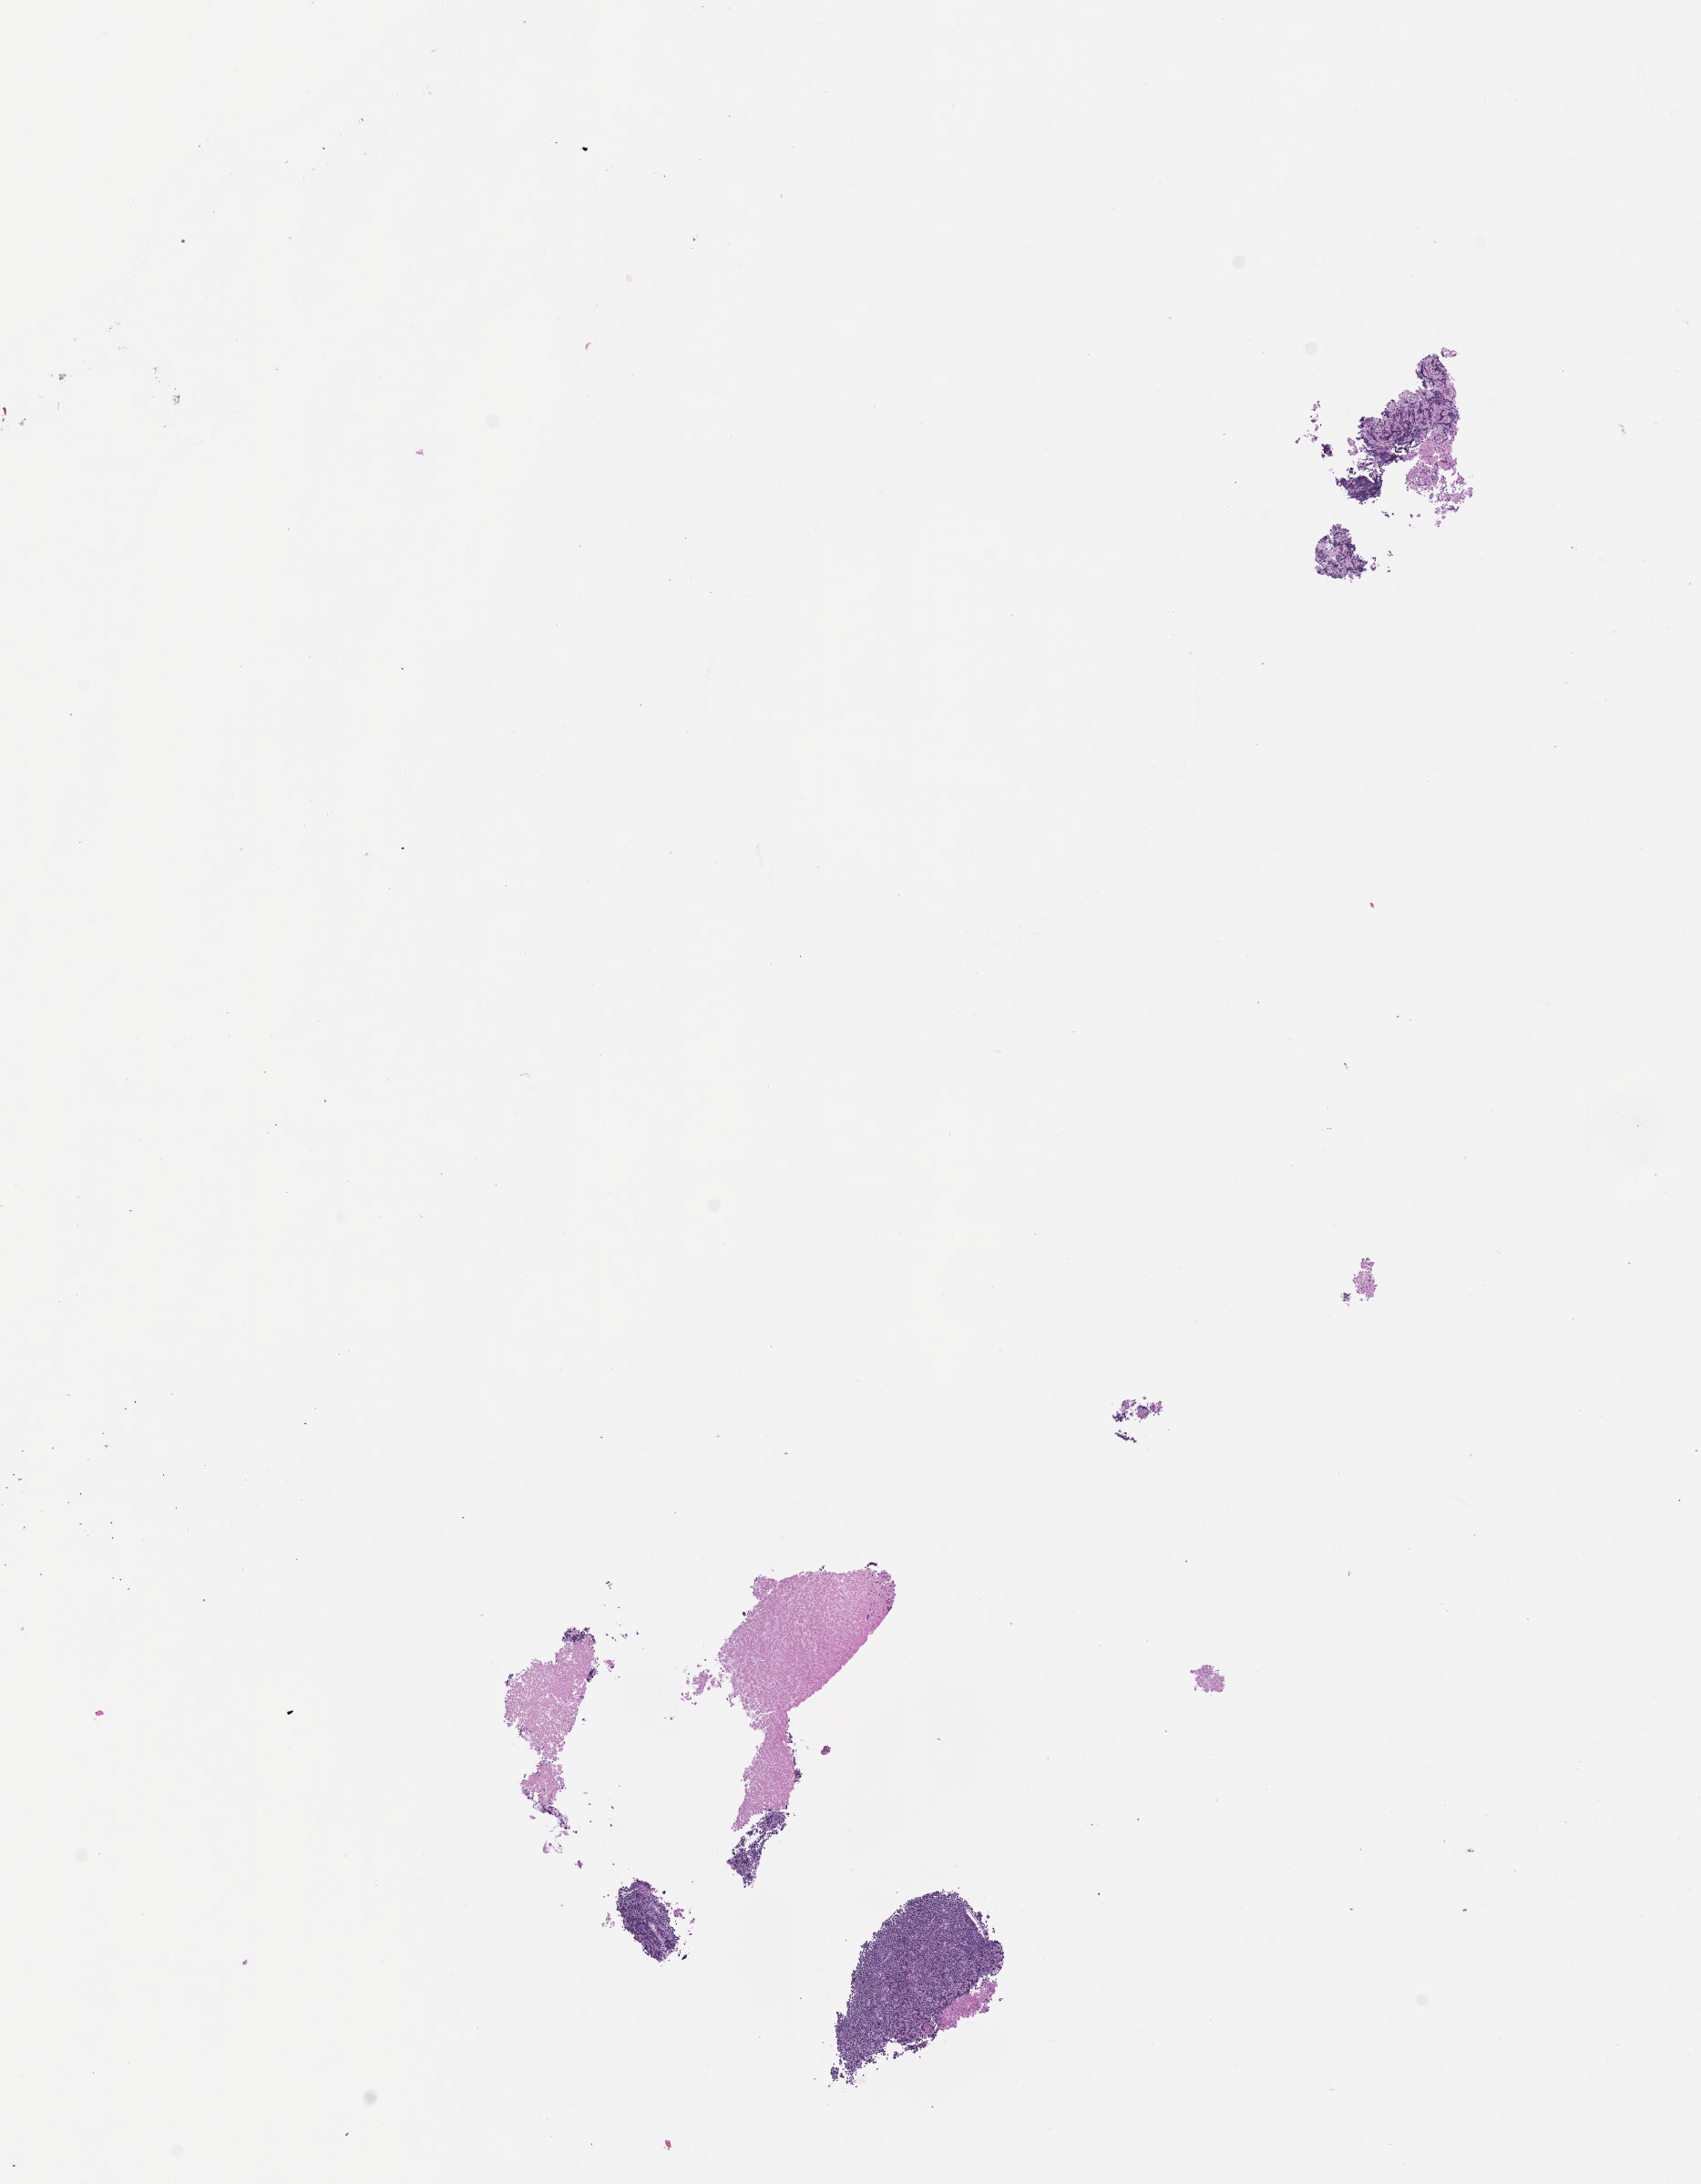
Whole-slide image, haematoxylin and eosin stain, shown as a low-resolution overview of the whole scanned area (about 7.5 x 9.7 mm); tumor tissue; site: abdominal lymph node. Male, age 5 years at initial diagnosis.
Diagnosis: Diffuse large B-cell lymphoma, NOS.